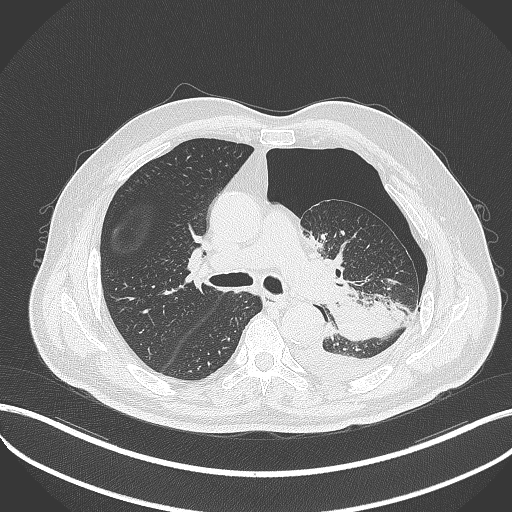
Chest CT, one axial slice; reconstruction kernel B70f; 120 kVp; lung window (W 1500 / L -600 HU); 512 × 512 image matrix, field of view 400 × 400 mm. Male patient, age 76 years. Case-level facts recorded for this patient, not image findings: clinical TNM (as recorded): T3 N0 M1b.
Annotated regions visible in this slice (bounding box drawn by a radiologist):
- lung tumour (recorded histology: adenocarcinoma): bounding box [x1, y1, x2, y2] px = [326, 290, 401, 343]